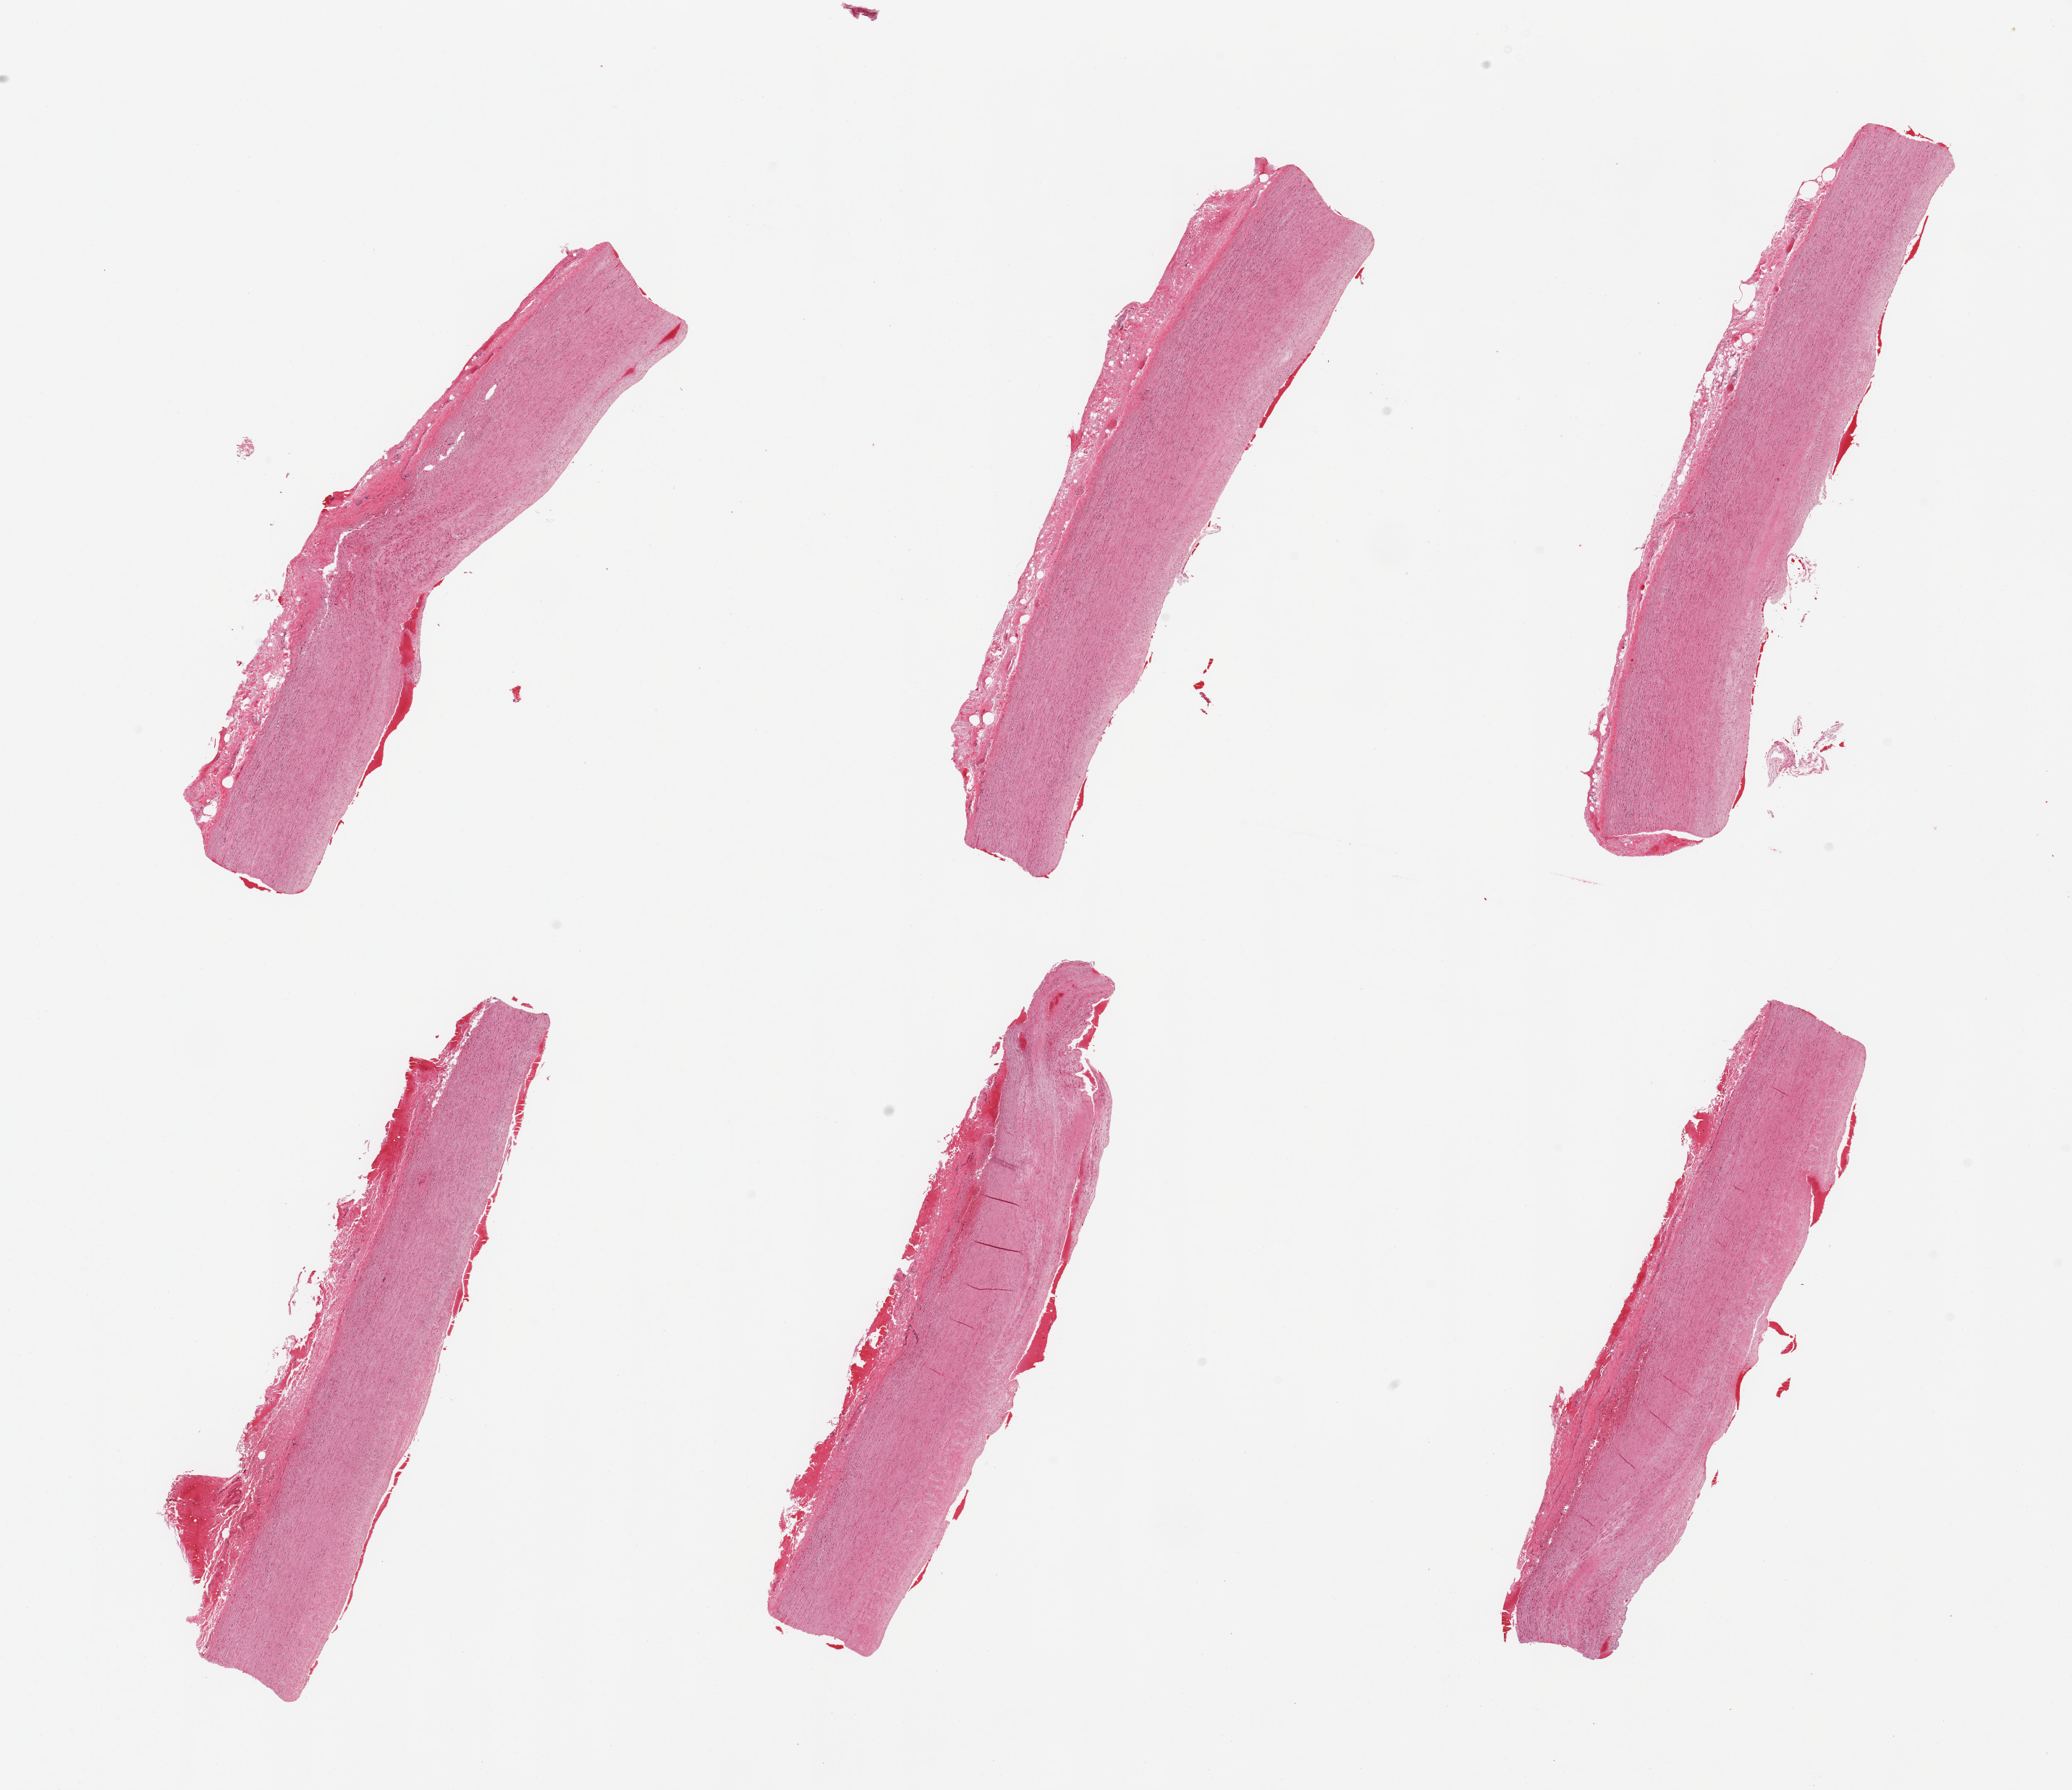
Digitized H&E-stained section, brightfield — shown as a low-resolution overview of the whole scanned area (about 22.6 x 19.6 mm), PAXgene-fixed, paraffin-embedded tissue, sampled site (target tissue): aorta, tissue donor sample. Donor sex: male.
• pathologist's review note for this sample: 6 pieces, minimal atherosis